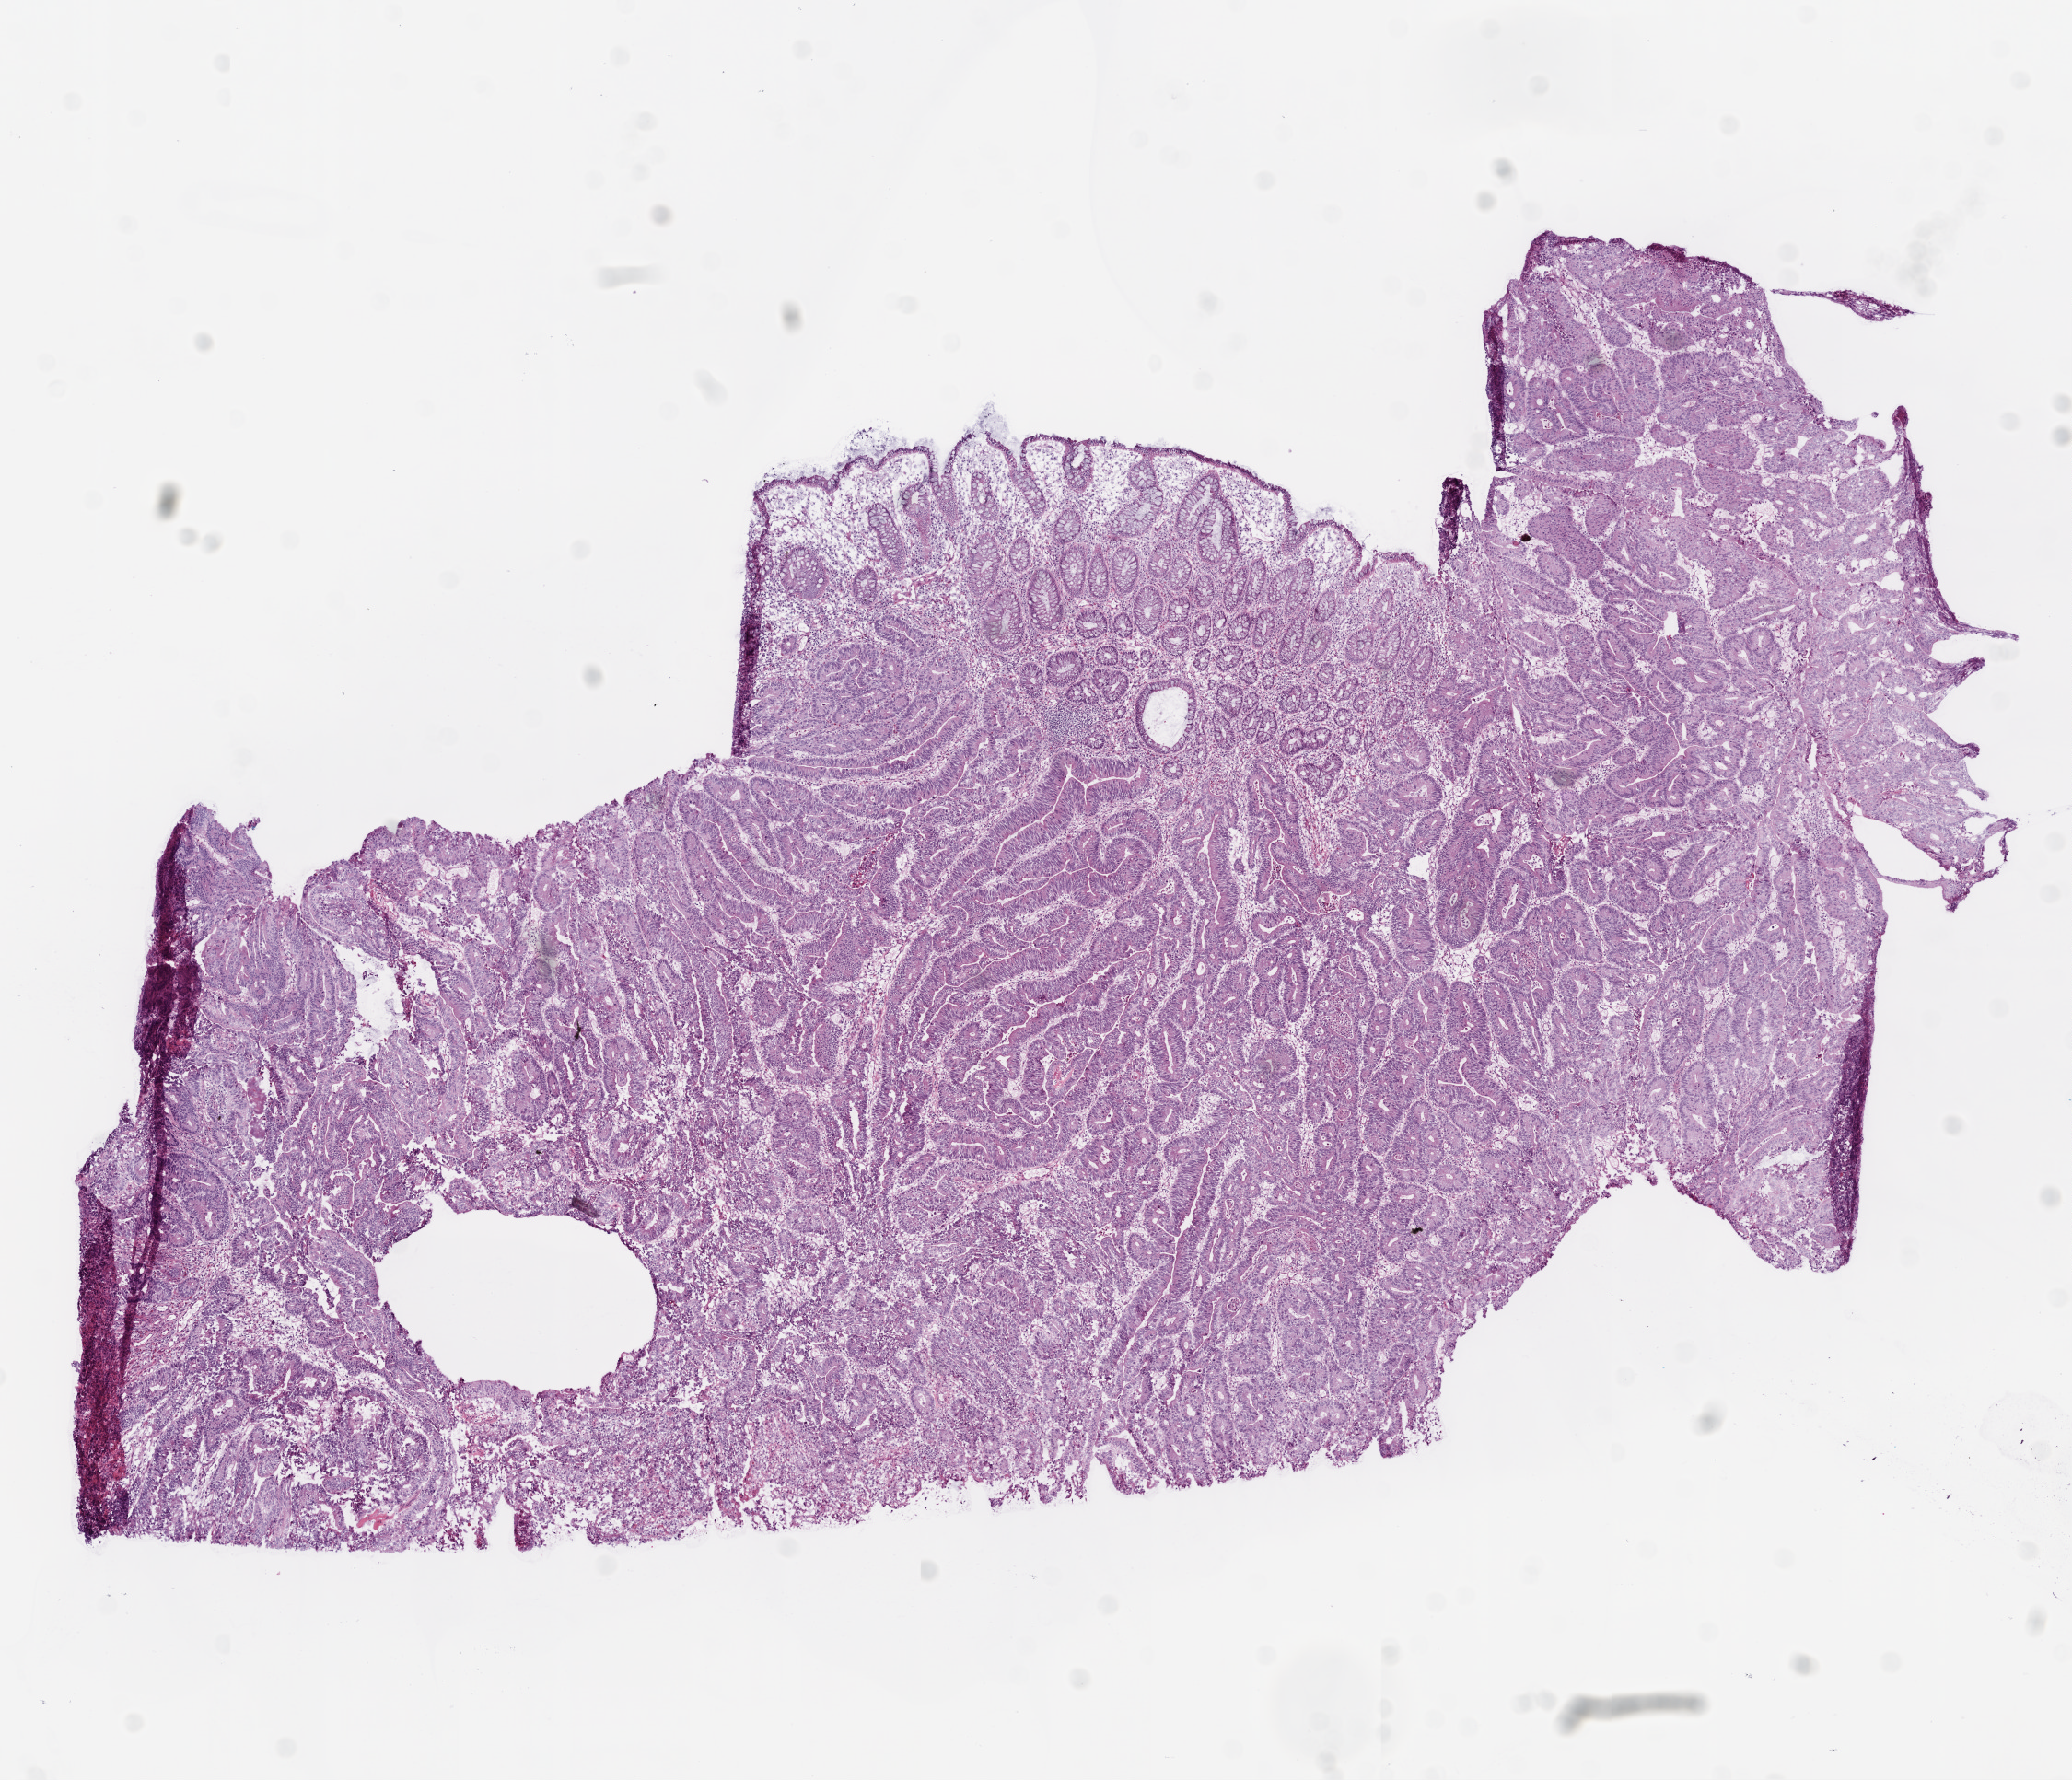
Hematoxylin and eosin (H&E) stained whole-slide image — a low-resolution overview of the entire scanned area, about 9.0 x 7.8 mm. Frozen section from the top of the tissue portion. Rectum, primary tumour sample. Female, age 71 years at initial diagnosis.
Pathologic diagnosis: Adenocarcinoma, NOS.